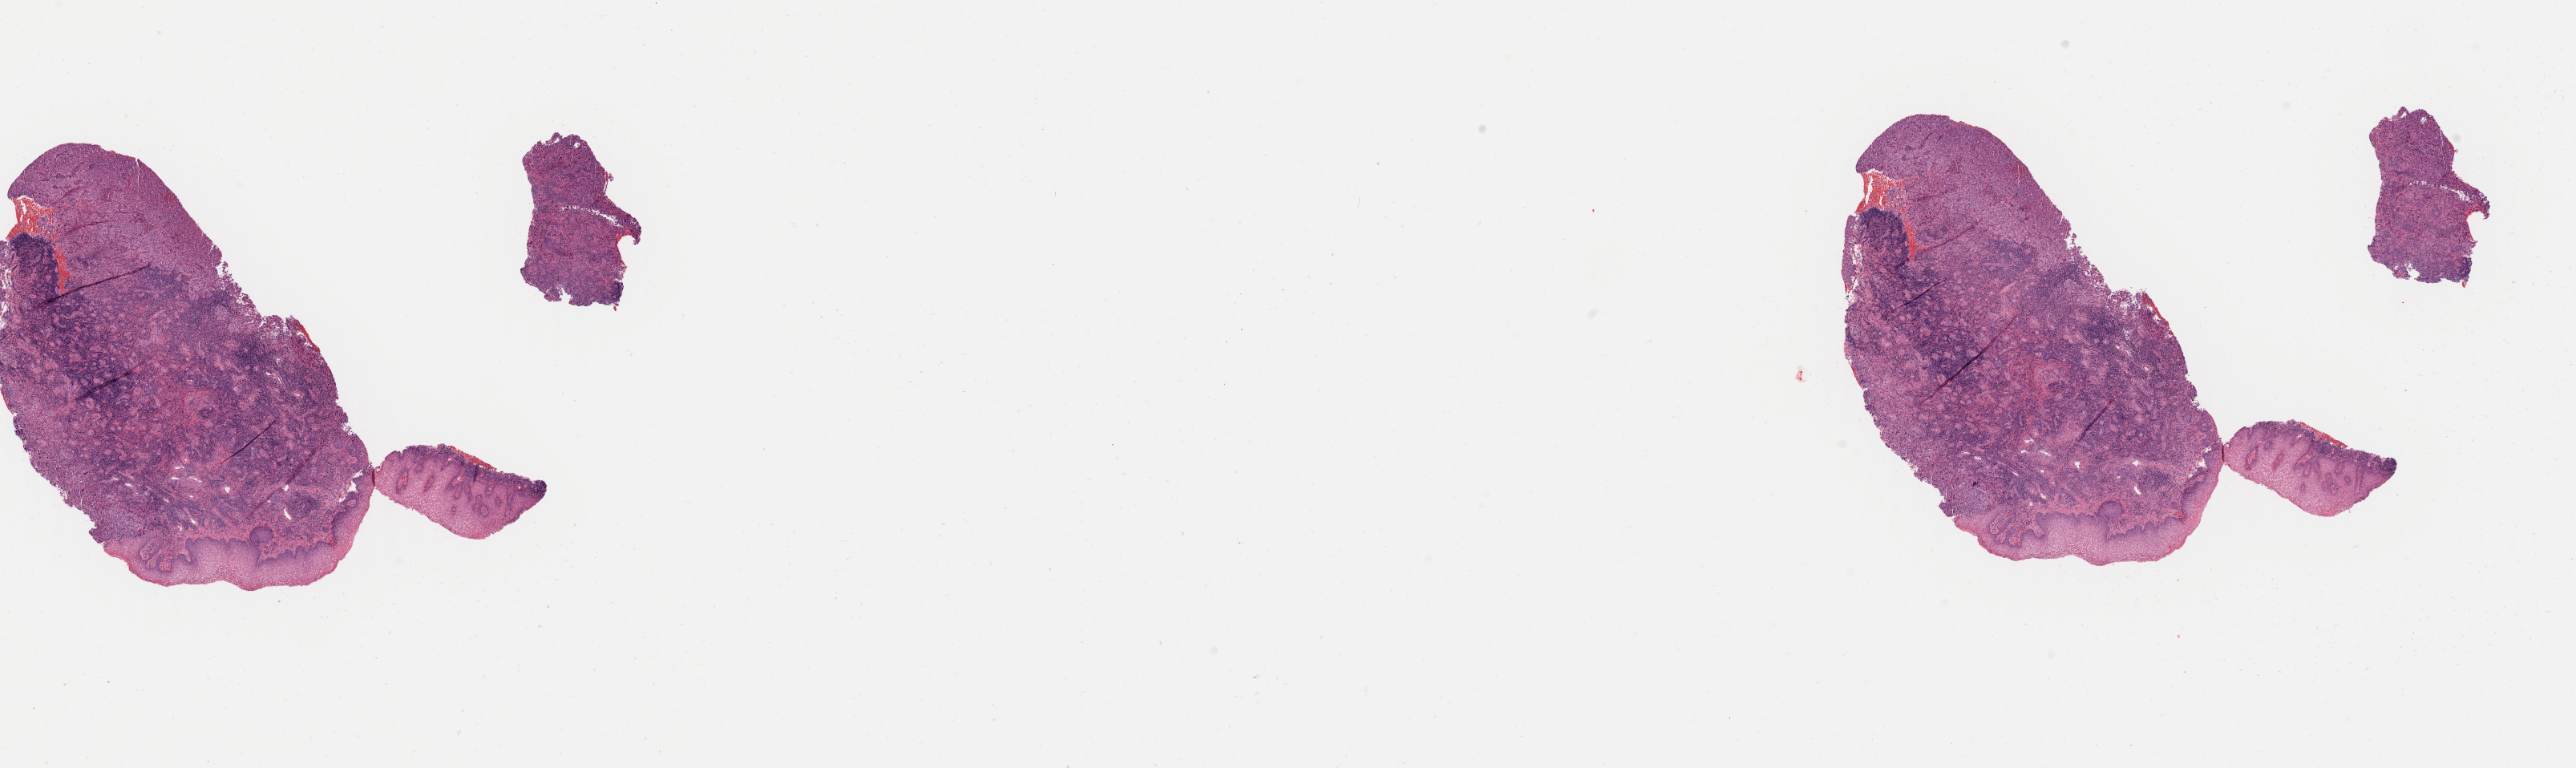
Haematoxylin and eosin whole-slide image, low-resolution overview of the scanned area, about 25.6 x 7.6 mm; tumor tissue; anatomic site: cervix. Patient female; aged 29.
• histologic diagnosis: Squamous cell carcinoma, large cell, nonkeratinizing, NOS